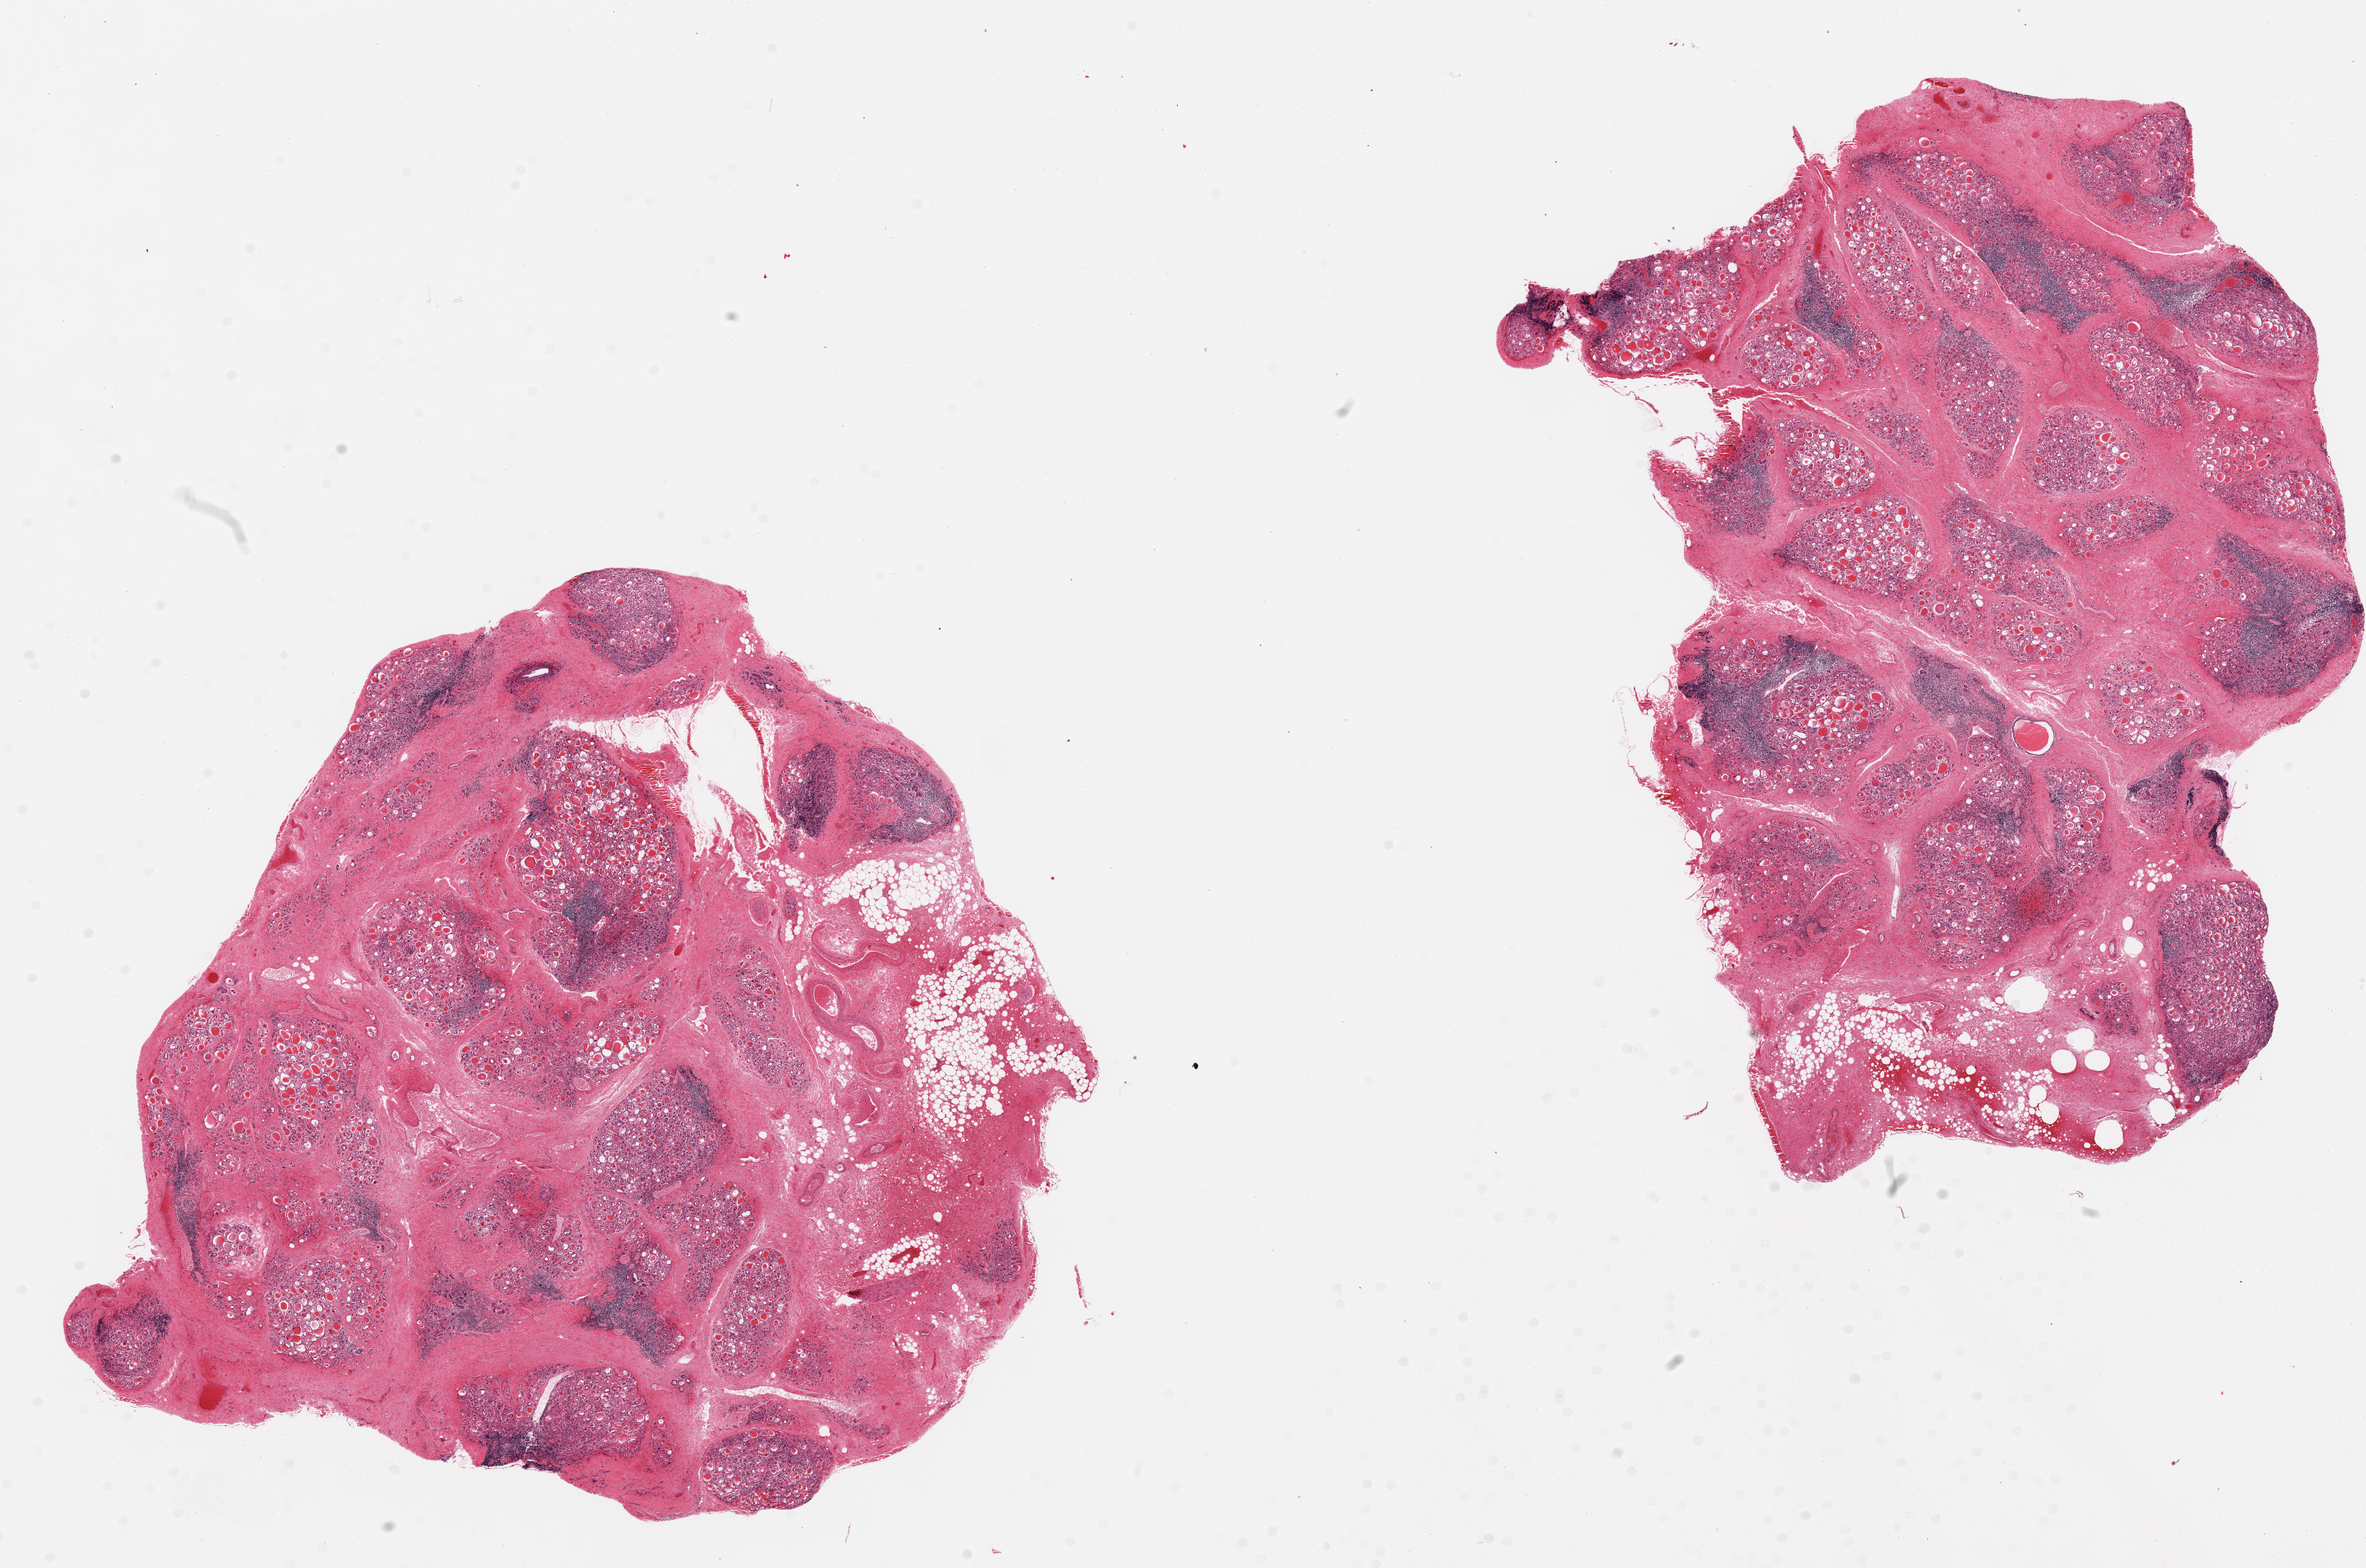
Haematoxylin and eosin whole-slide image, brightfield, shown as a low-resolution overview of the whole scanned area (about 24.6 x 16.3 mm). PAXgene-fixed, paraffin-embedded tissue. Section of thyroid (target tissue). Tissue donor sample. Donor: male.
• review note (as recorded): 2 pieces; Hashimoto thyroiditis with moderate fibrosis; each has 20% peripheral fat